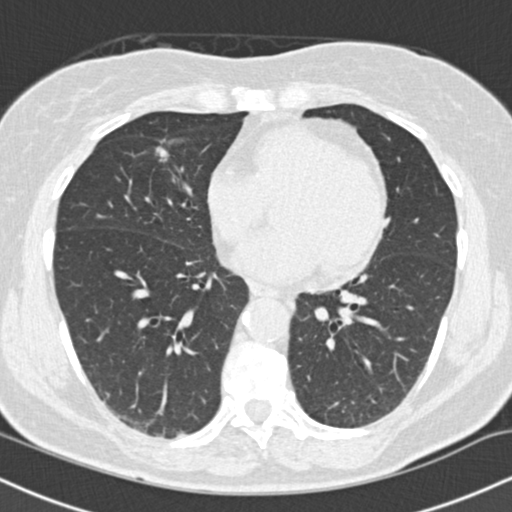
Low-dose screening chest CT, one axial slice; lung window (W 1500 / L -600 HU); 512 × 512 image matrix, field of view 320 × 320 mm.
Outlined on this slice (manually delineated by an expert):
- lesion 1 (tumor, middle lobe of right lung): bounding box [x1, y1, x2, y2] px = [156, 146, 169, 162]